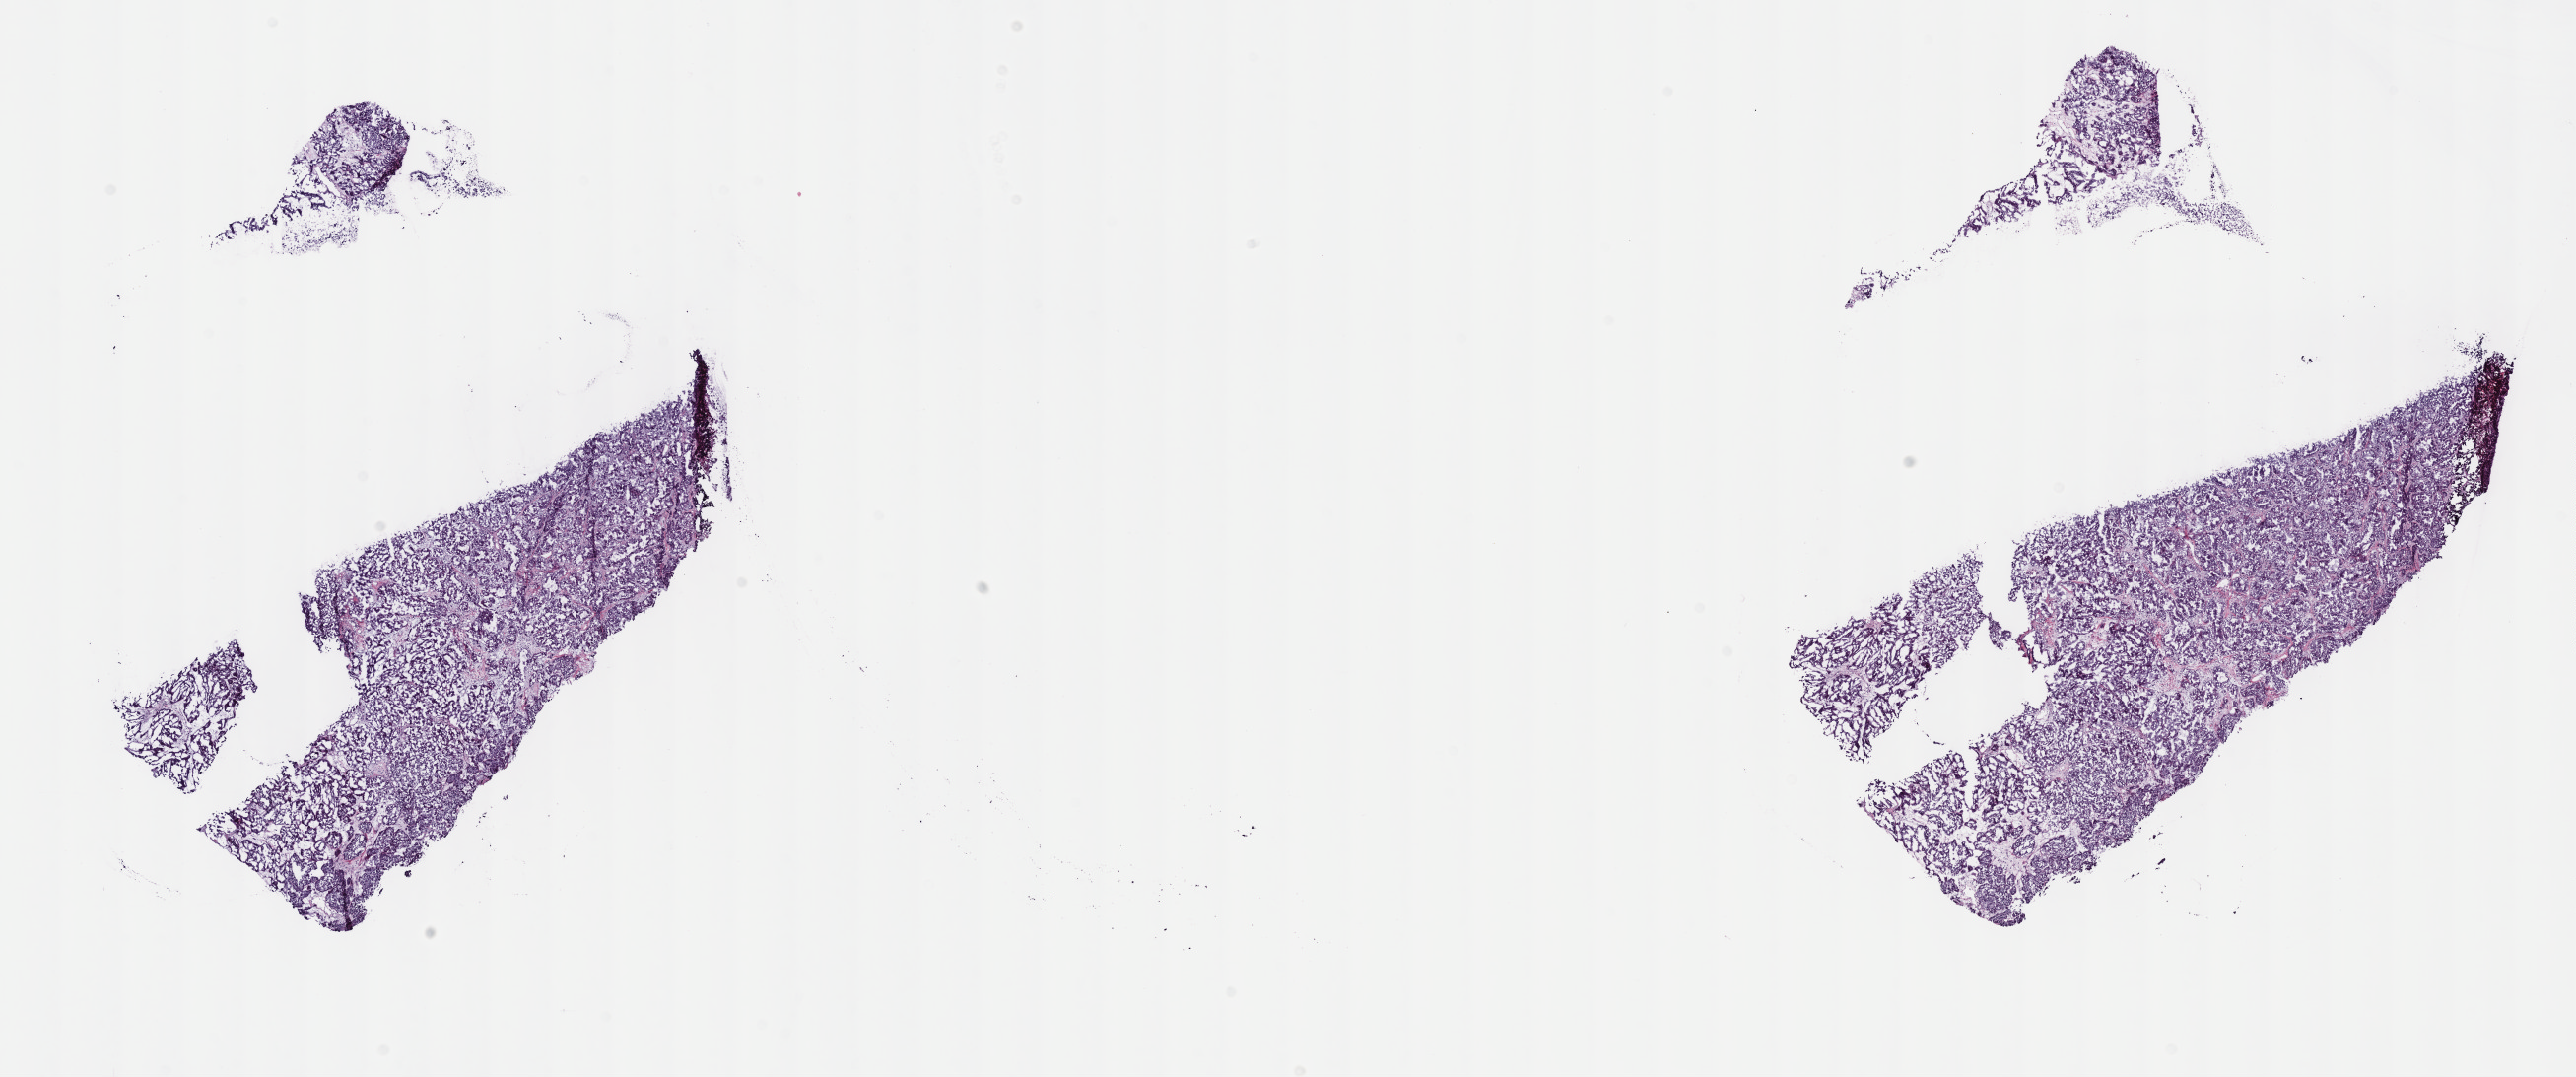
Digitized H&E-stained tissue section (whole slide) — a low-resolution overview of the entire scanned area, about 21.1 x 8.8 mm (slide scanned at 40x). Frozen section from the top of the tissue portion. Kidney, primary tumour sample. Patient: male, age at initial diagnosis 69 years. Slide review estimates, as recorded: tumour cells 75%, tumour nuclei 75%, normal cells 0%, stromal cells 25%, necrosis 0%. Infiltration values recorded for this section: lymphocyte infiltration 3%, monocyte infiltration 4%, neutrophil infiltration 1%.
• AJCC pathologic stage: I (7th edition)
• diagnosis: Papillary adenocarcinoma, NOS